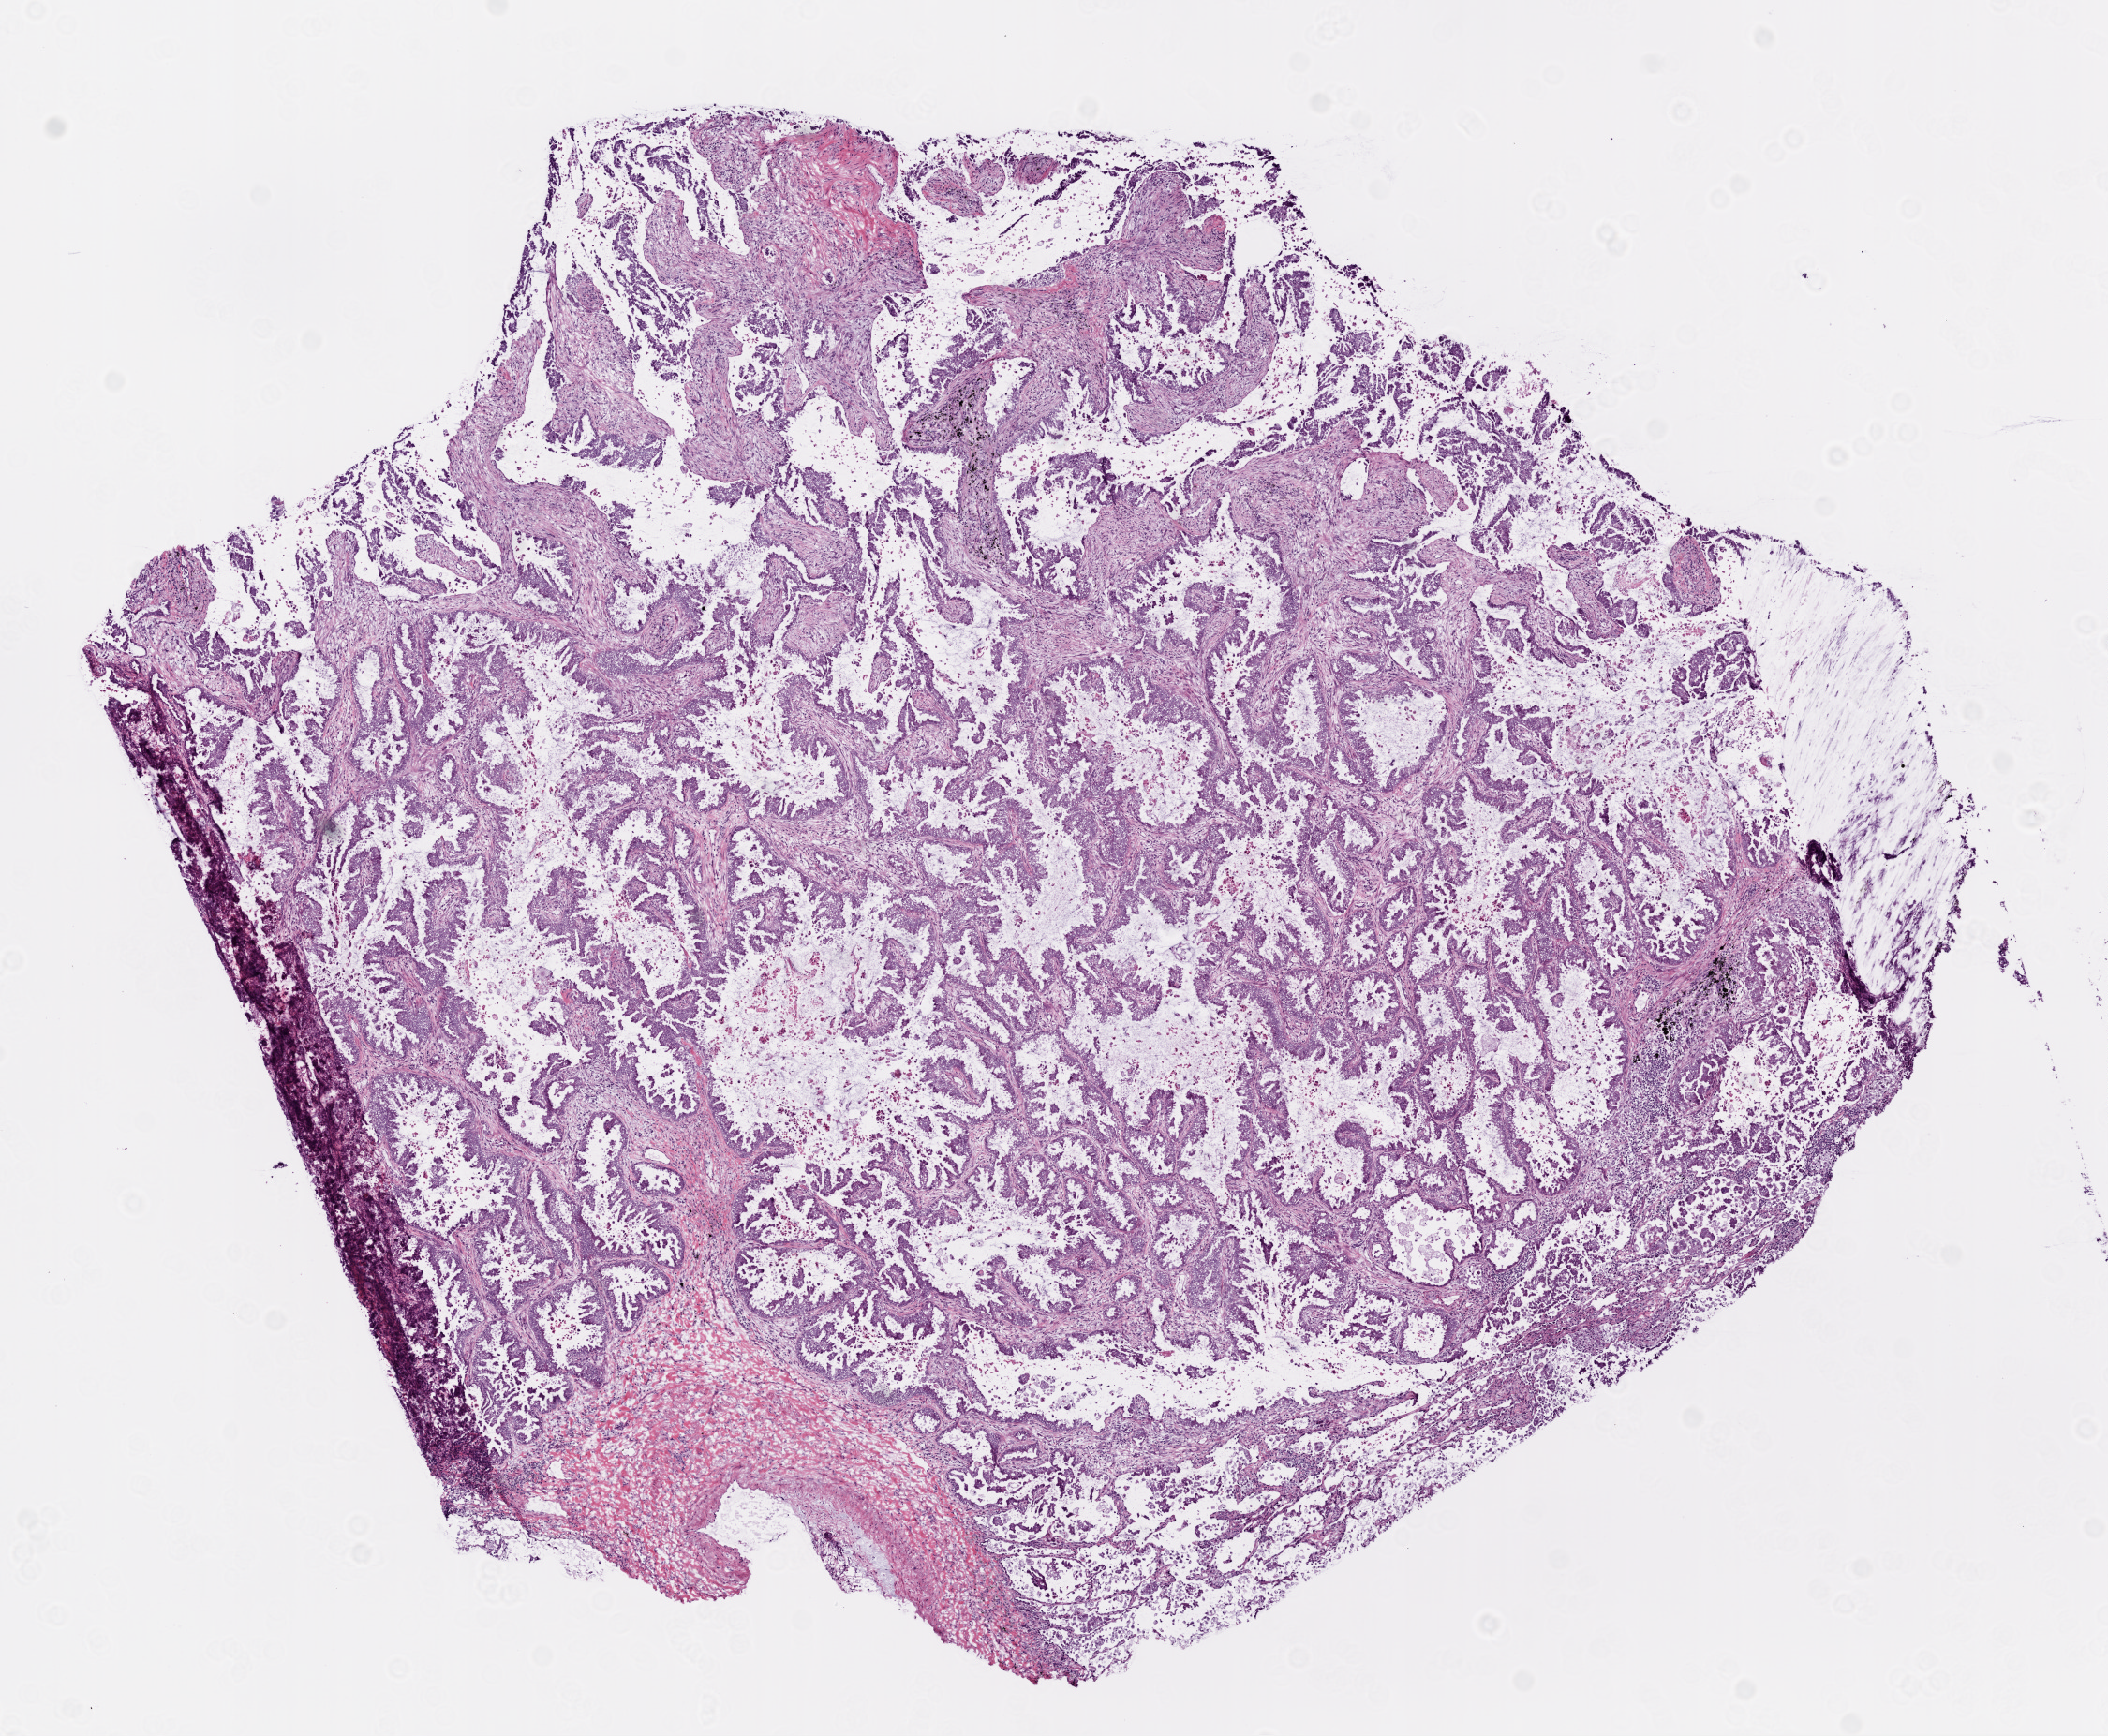
H&E-stained whole-slide image, shown as a low-resolution overview of the whole scanned area (about 9.0 x 7.4 mm, slide scanned at 20x), frozen section from the bottom of the tissue portion, lung, primary tumour sample. Female, age 69 years at initial diagnosis. Slide review estimates, as recorded: tumour cells 90%, tumour nuclei 75%.
Histologic diagnosis: Adenocarcinoma with mixed subtypes.